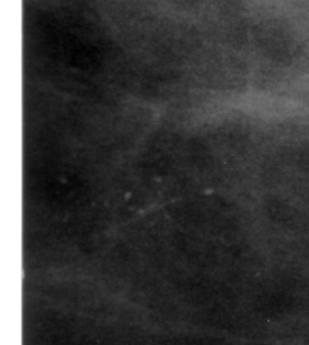
Crop from a digitized film mammogram around one marked abnormality, left breast, CC view.
Finding: calcifications, morphology pleomorphic, distribution clustered; BI-RADS assessment category 0 (incomplete: needs additional imaging); subtlety rating 3 on a 1 (subtle) to 5 (obvious) scale; pathology (as recorded): malignant.